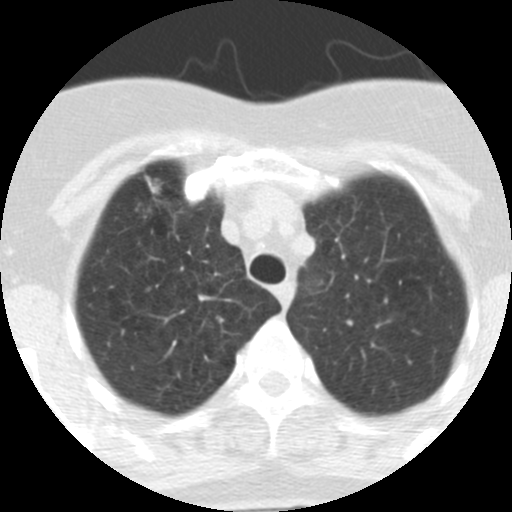
Chest CT (low-dose screening protocol), one axial image. Baseline screening round. Lung window (W 1500 / L -600 HU). 2.5 mm slice thickness. Slice 59 of 313 in the series. Female, age 62 years at enrolment. Current smoker at enrolment.
Lesion marked by an expert reader, bounding box (x1, y1, x2, y2) in pixels: (116, 172, 190, 238). Screening reader's record for this exam (one nodule recorded; not confirmed to be the boxed lesion): non-calcified nodule or mass ≥4 mm, right upper lobe, 9 × 7 mm, spiculated (stellate) margins, soft tissue attenuation. Participant outcome: lung cancer diagnosed 126 days after this screen — adenocarcinoma, NOS, right upper lobe, moderately differentiated (G2), stage IA (AJCC 6th edition), 18 mm at pathology.